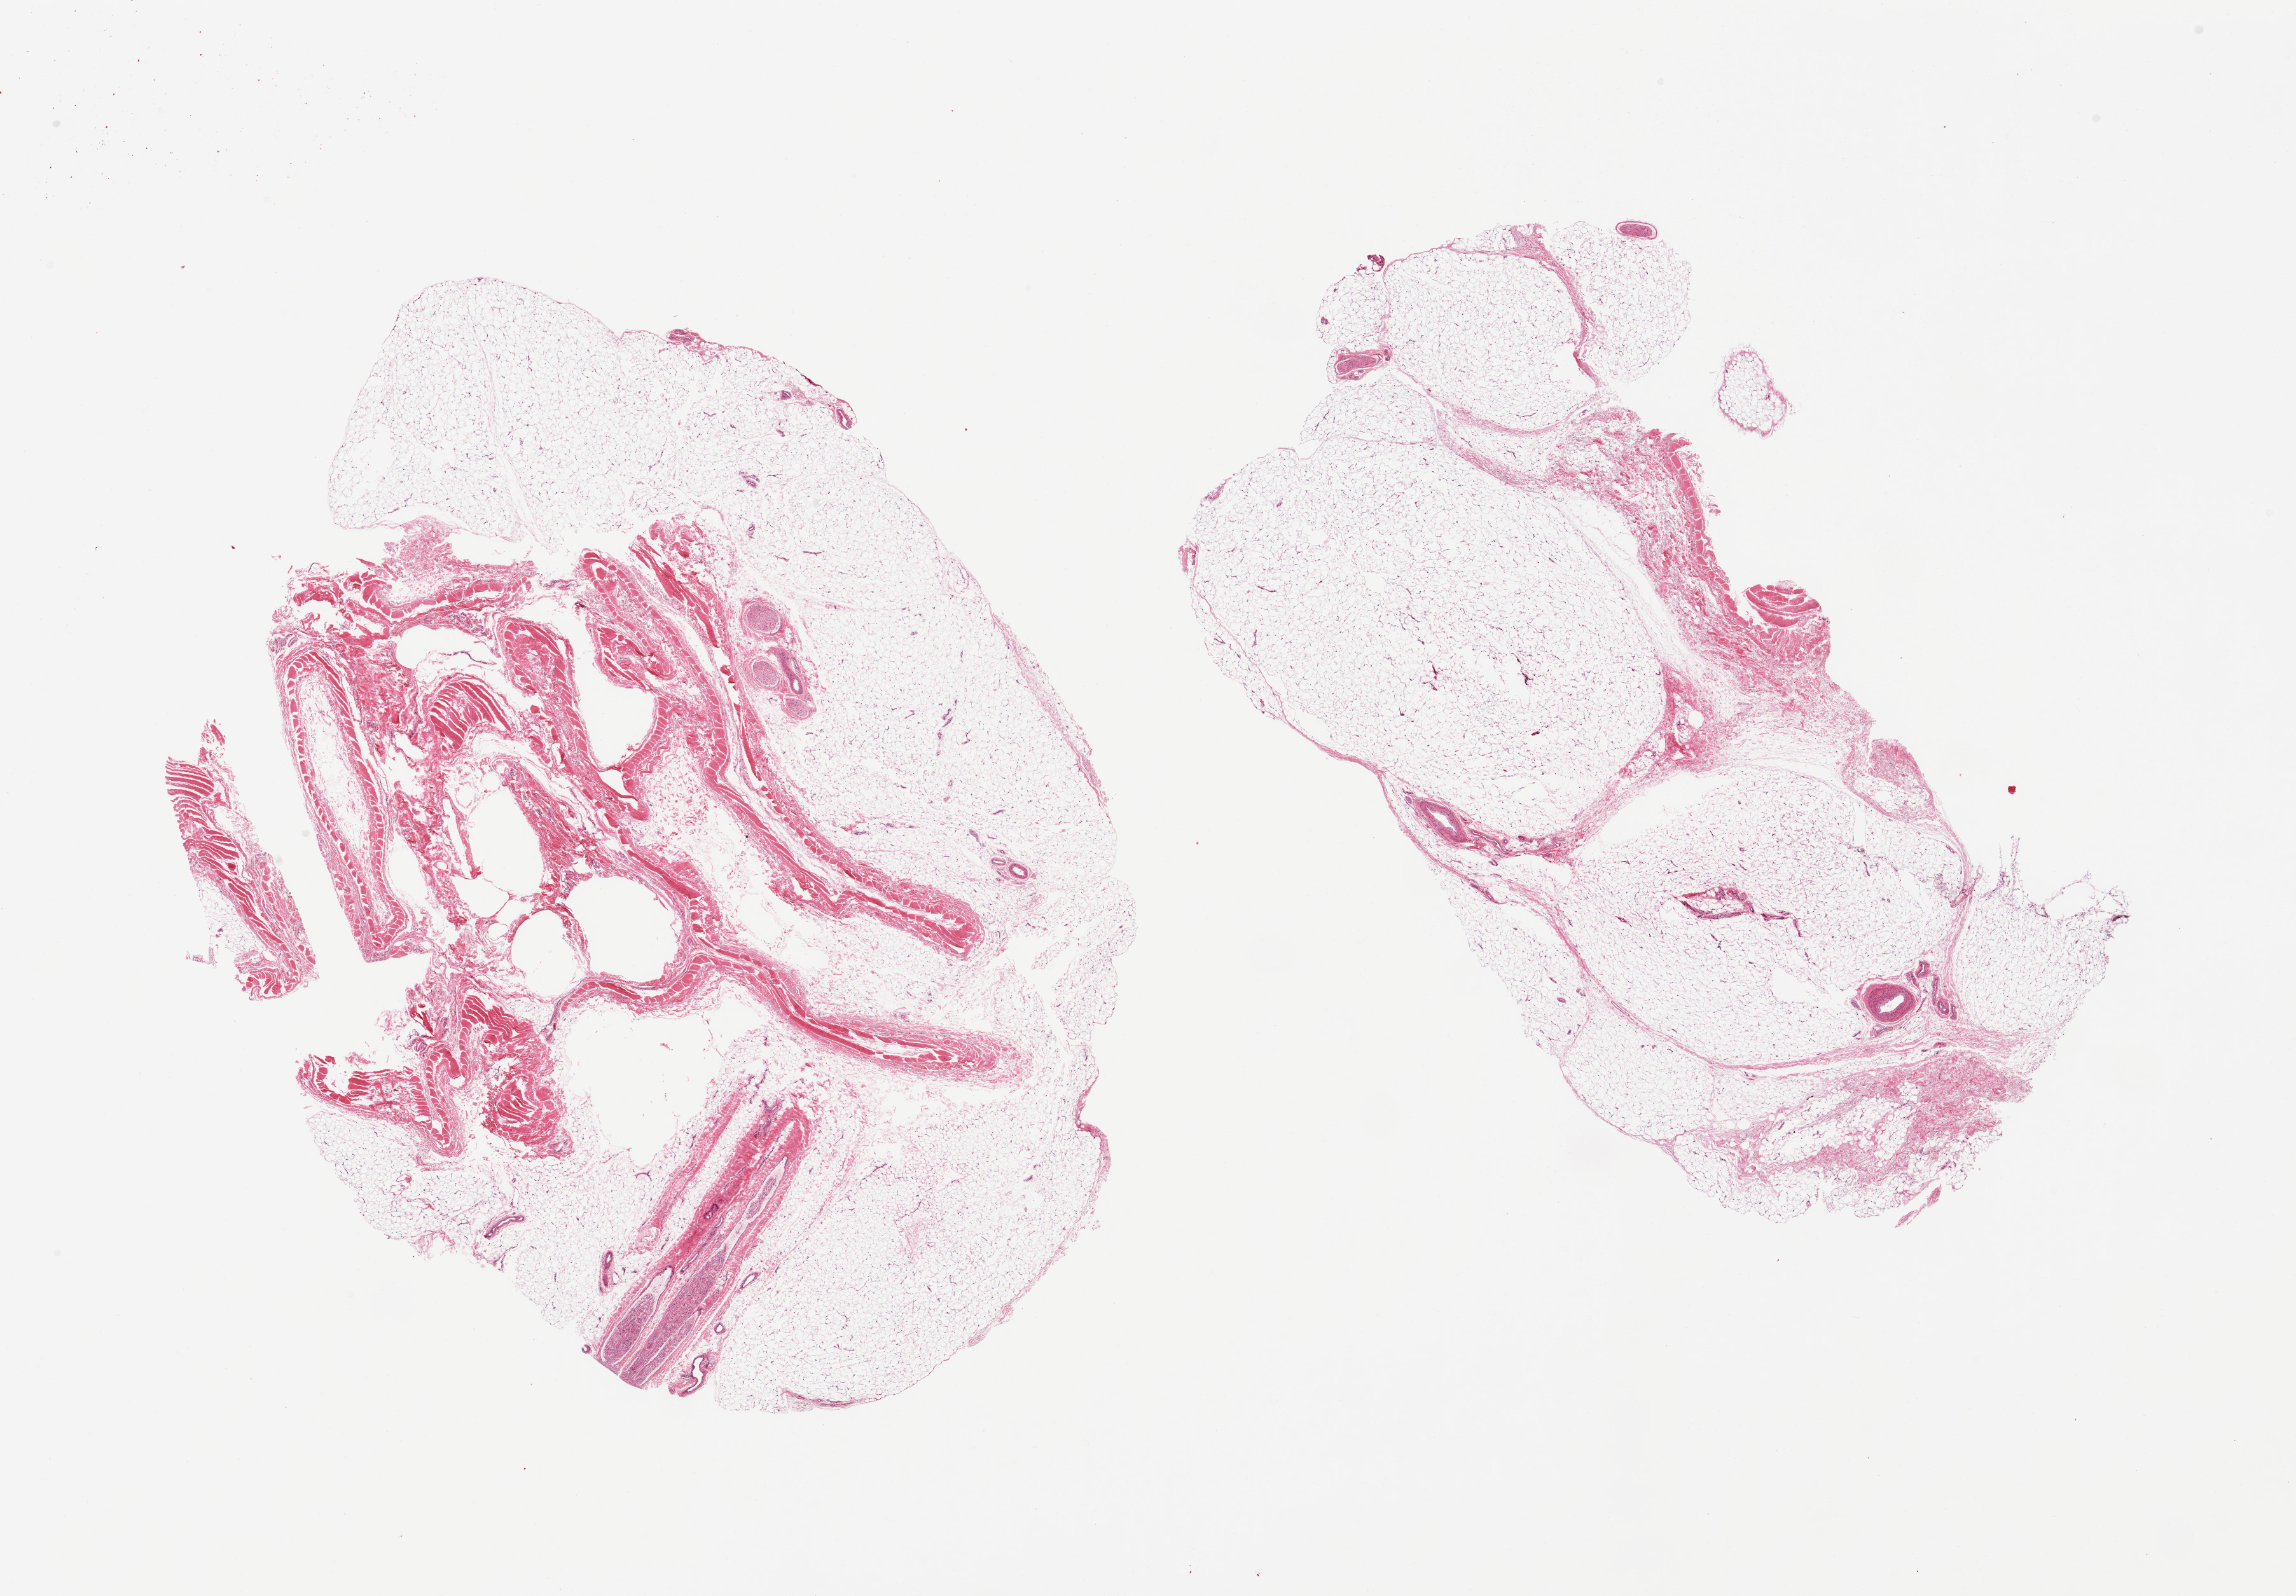
Hematoxylin and eosin (H&E) whole-slide image — whole scanned area (about 28.5 x 19.8 mm) shown as a low-resolution overview; PAXgene-fixed paraffin-embedded (PFPE) section; sampled site (target tissue): adipose tissue; tissue donor sample. Female donor.
- pathologist's review note for this sample: 2 pieces; high (50%) collagen (fascia) content, especially in 1 piece